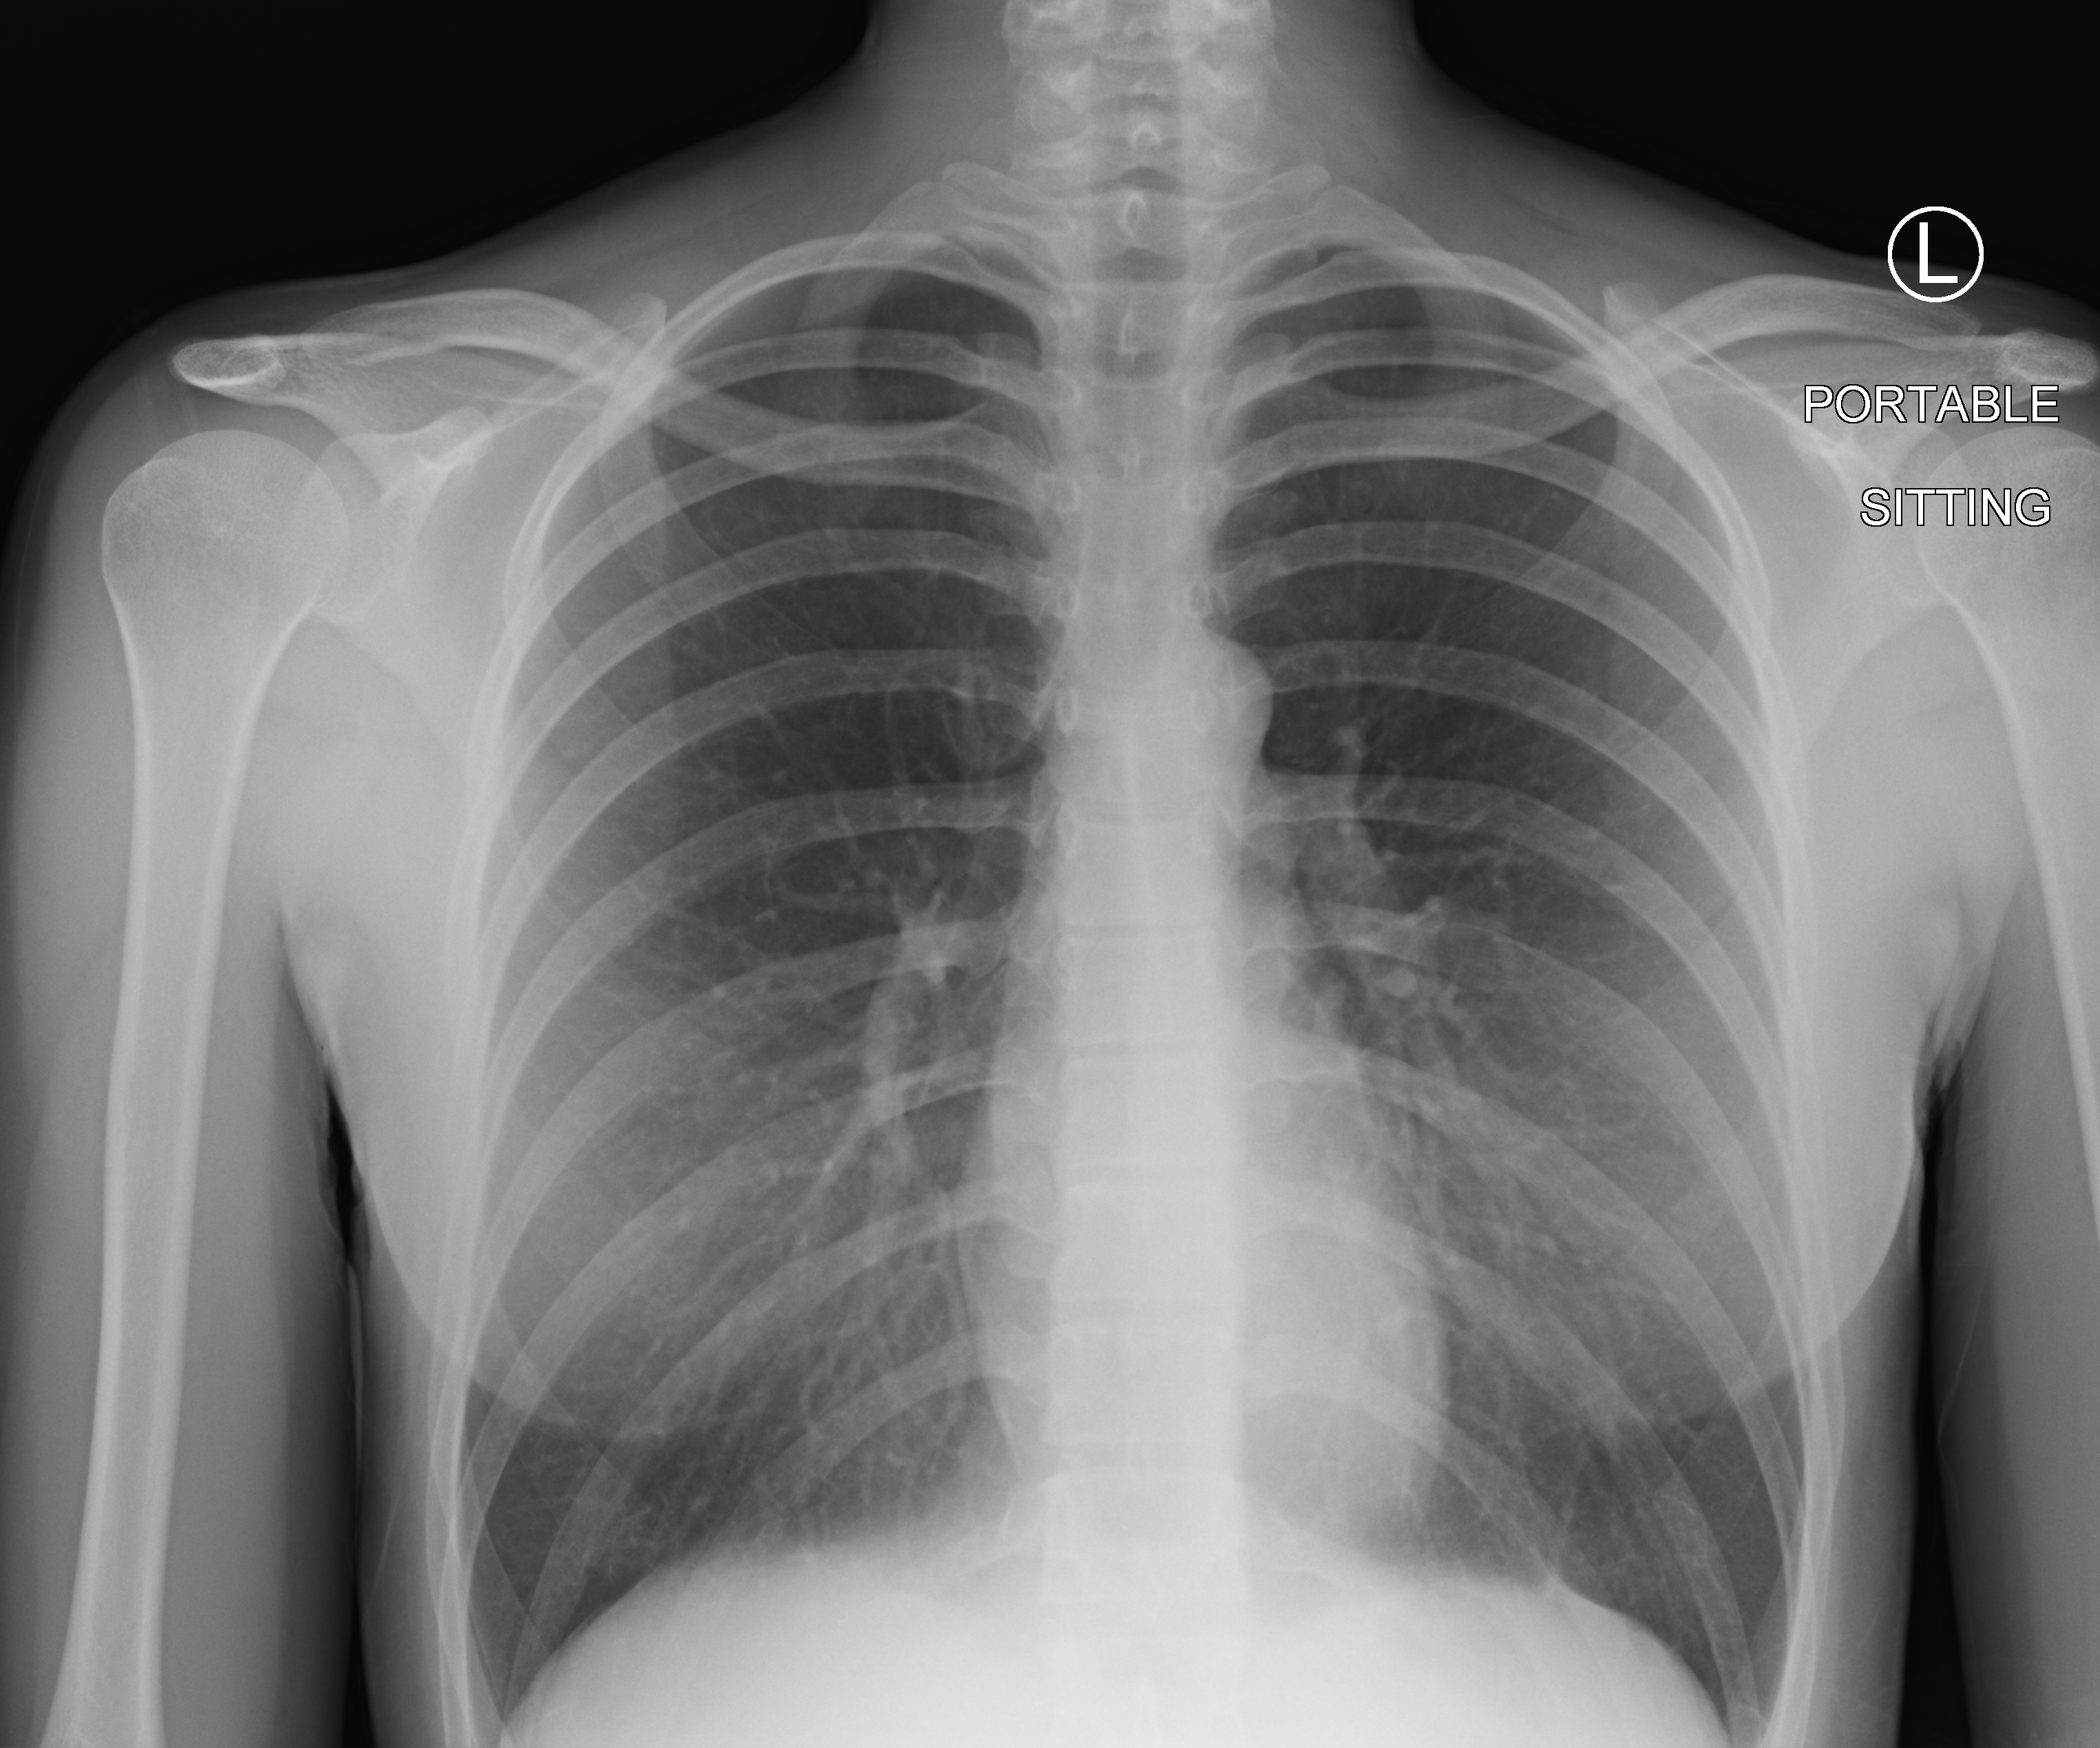
Portable chest radiograph, anteroposterior (AP) projection. Patient hospitalised with COVID-19; female, aged 18–59 years.
From the hospital-stay record, not from the radiograph (when in the stay this image was taken is not recorded): admitted to intensive care during this hospital stay: no; mechanically ventilated during this hospital stay: no.